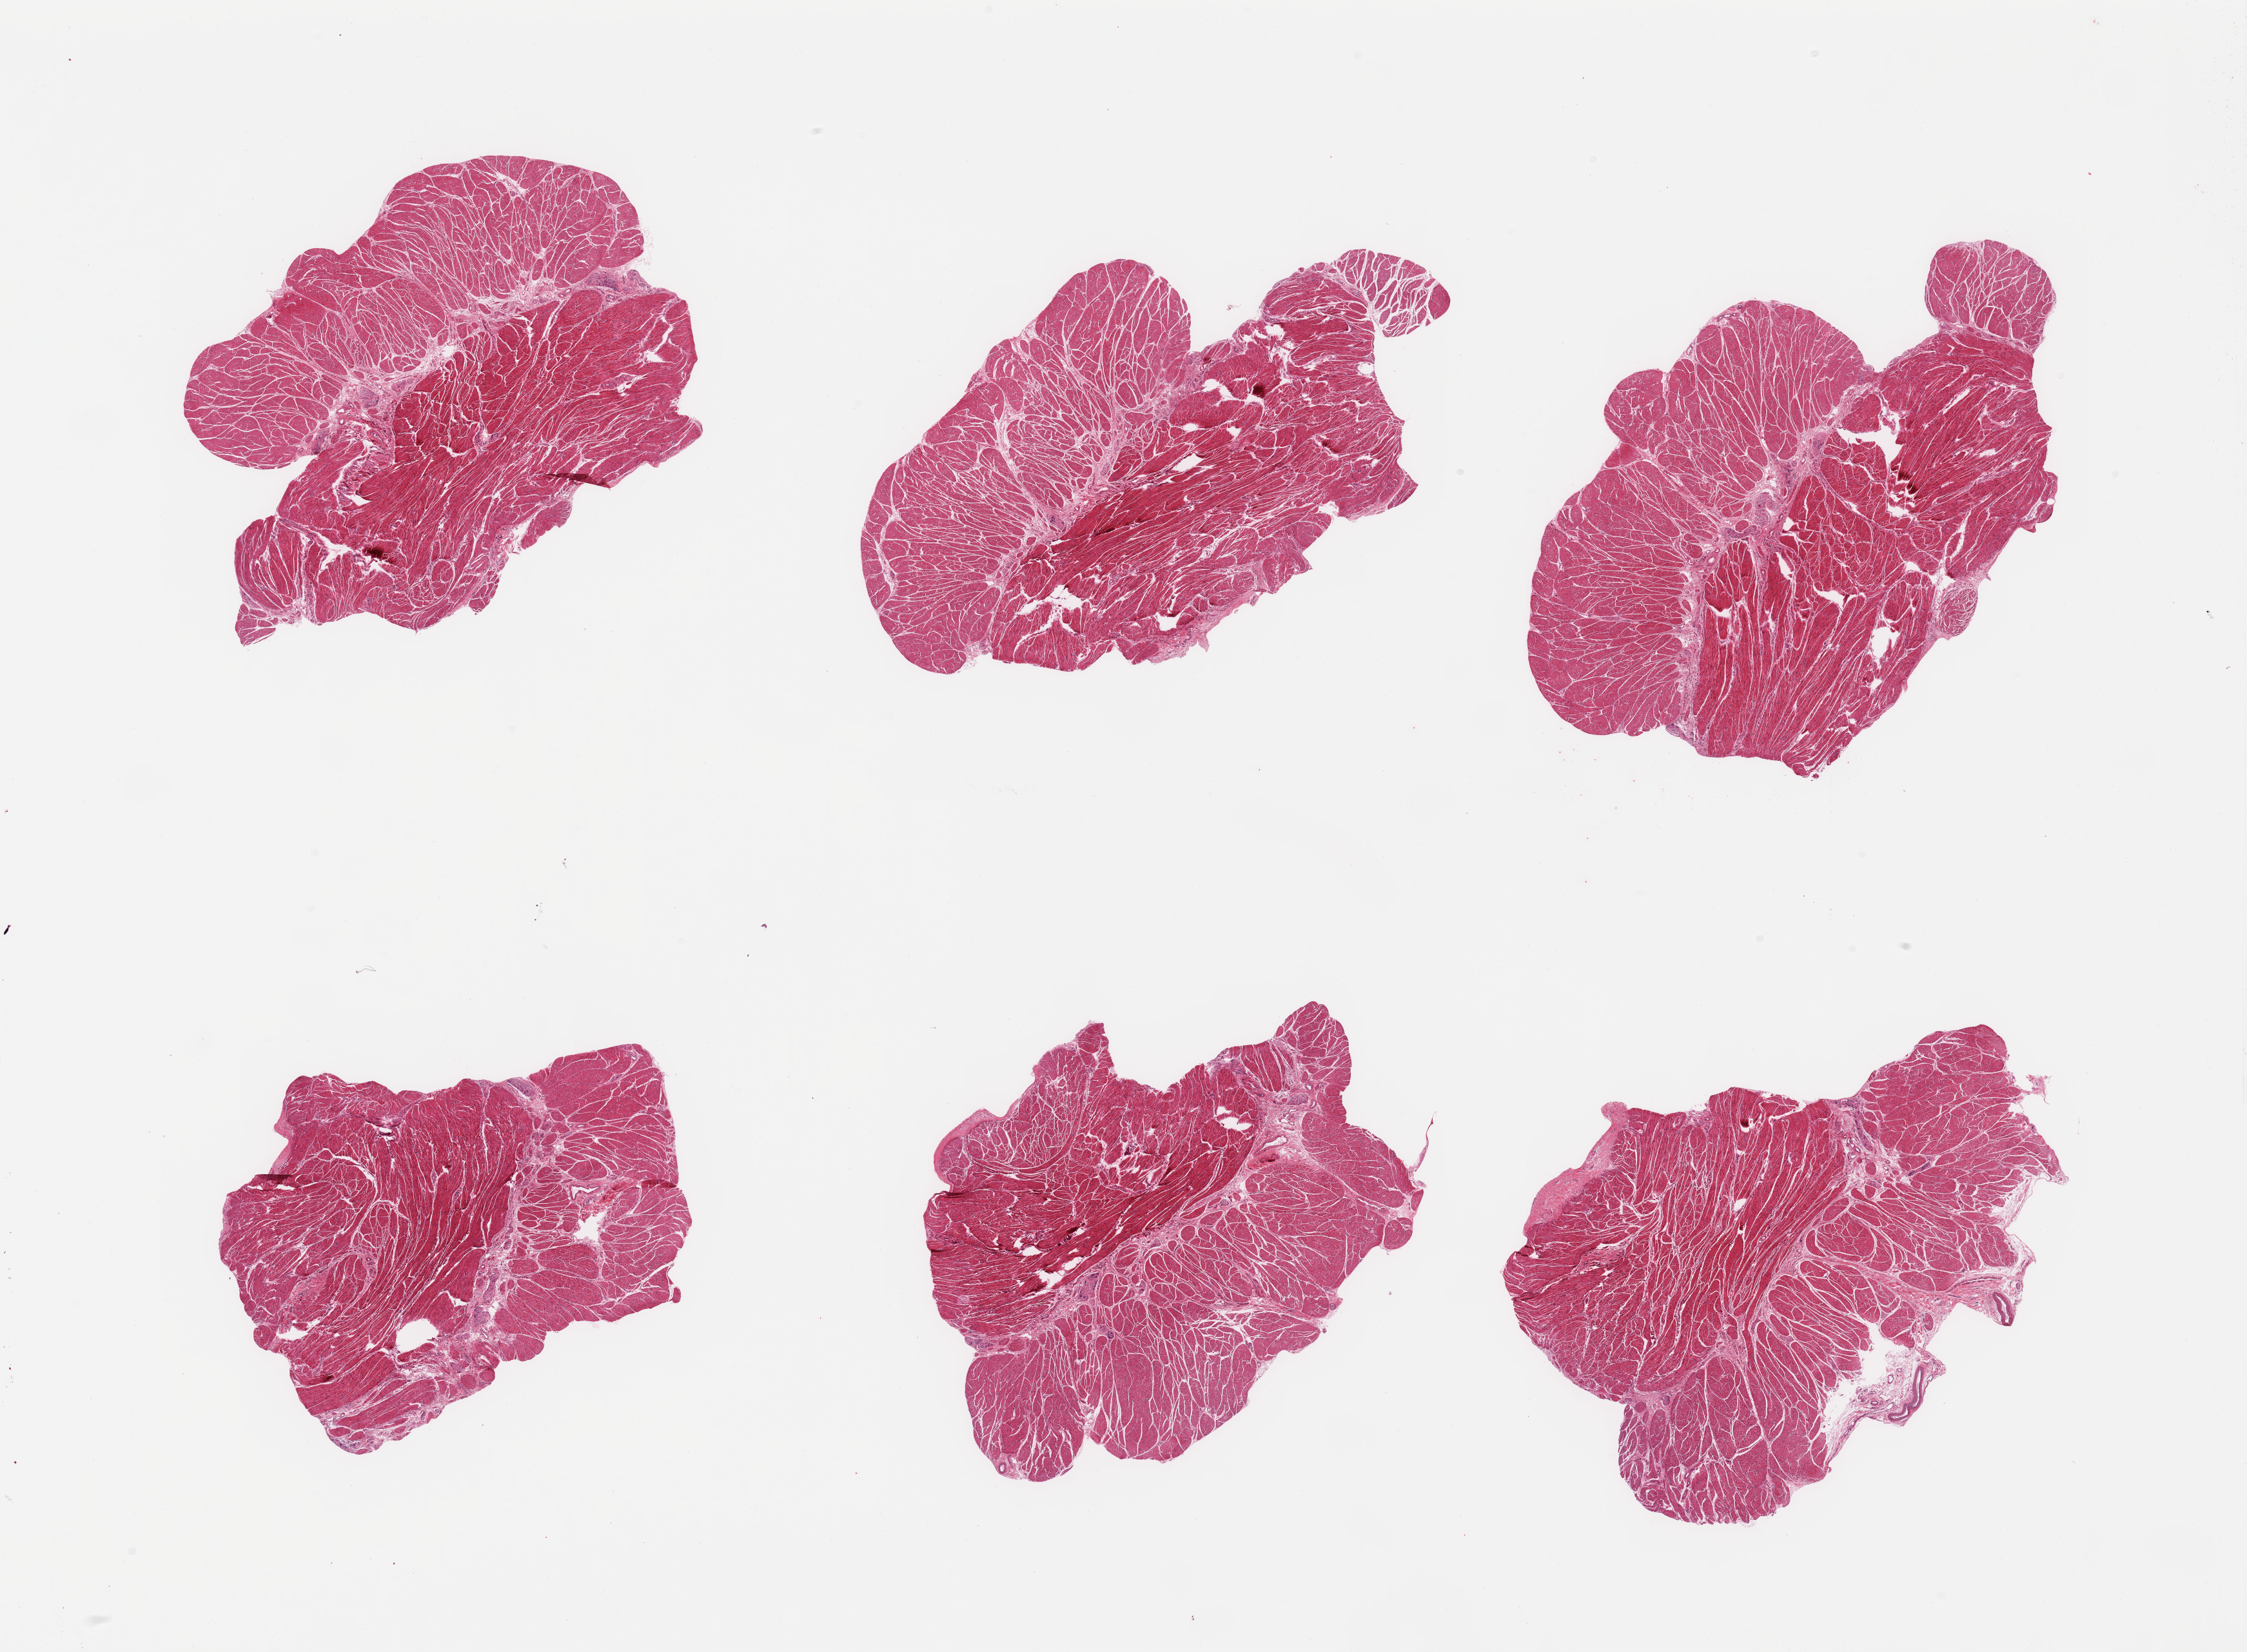
Digitized hematoxylin and eosin (H&E)-stained section, a low-resolution overview of the entire scanned area, about 27.6 x 20.3 mm. PAXgene-fixed paraffin-embedded (PFPE) section. Sampled site (target tissue): esophageal muscle. Tissue donor sample. Donor: male.
Reviewer comment on this tissue sample: 6 pieces, confirmed target muscularis.